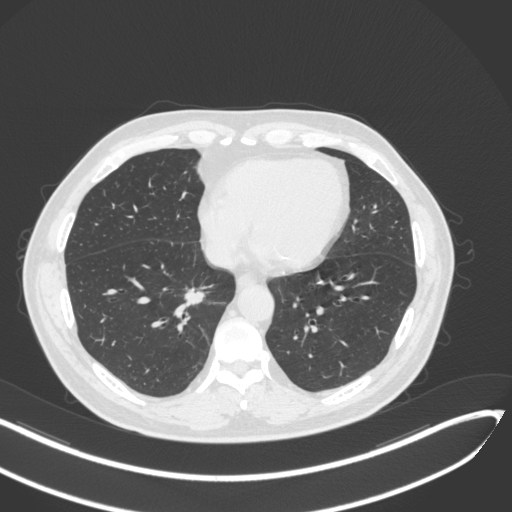
Chest CT, one axial slice. Position 132 of 429 along the scan axis. Lung window (W 1500 / L -600 HU). 1 mm slice thickness. 512 × 512 image matrix, field of view 400 × 400 mm. Patient: male, 62 years. From the clinical record (not read from this slice): clinical TNM (as recorded): T1b N0 M0; histopathological grade: G2.
Structures marked on this image (bounding box drawn by a radiologist):
- lung tumour (recorded histology: adenocarcinoma): bounding box (x1, y1, x2, y2) in pixels: (184, 286, 210, 309)